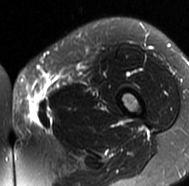
MRI of an extremity soft-tissue mass, one axial slice; slice 22 of 77 in the series (ordered by position); T2-weighted fat-saturated; MR volume resampled by the dataset authors to the PET/CT grid (not the native acquisition matrix); 3.27 mm slice thickness; 189 × 186 image matrix. Female patient. From the clinical record (not read from this slice): histological type: leiomyosarcoma; grade: high; site of the primary tumour: groin.
Outlined on this slice (expert contour drawn on MRI and transferred to this co-registered scan by the dataset authors):
- gross tumour volume including surrounding oedema: bounding box [x1, y1, x2, y2] px = [12, 68, 94, 135]